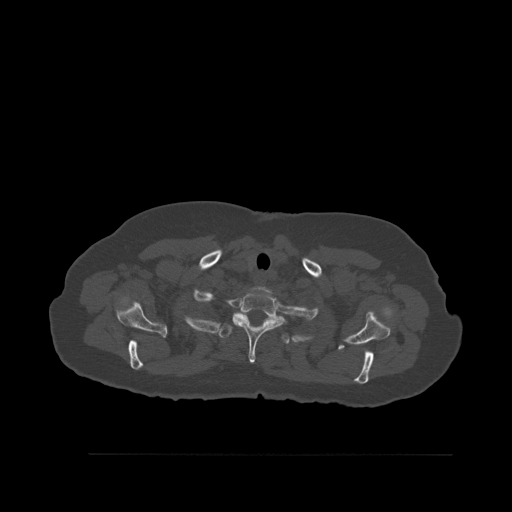
CT including the spine, one axial slice. Position 441 of 527 along the scan axis. Bone window (W 1800 / L 400 HU). 1.5 mm slice thickness. 512 × 512 image matrix. Female patient, age 73 years. From the clinical record (not read from this slice): primary cancer: breast; vertebrae with lytic lesions (as recorded): L2.
Outlined on this slice (semi-automatic segmentation, software-assisted and operator-edited):
- T1 vertebra: bounding box [x1, y1, x2, y2] px = [233, 289, 285, 364]
- T2 vertebra: [221, 318, 289, 345]